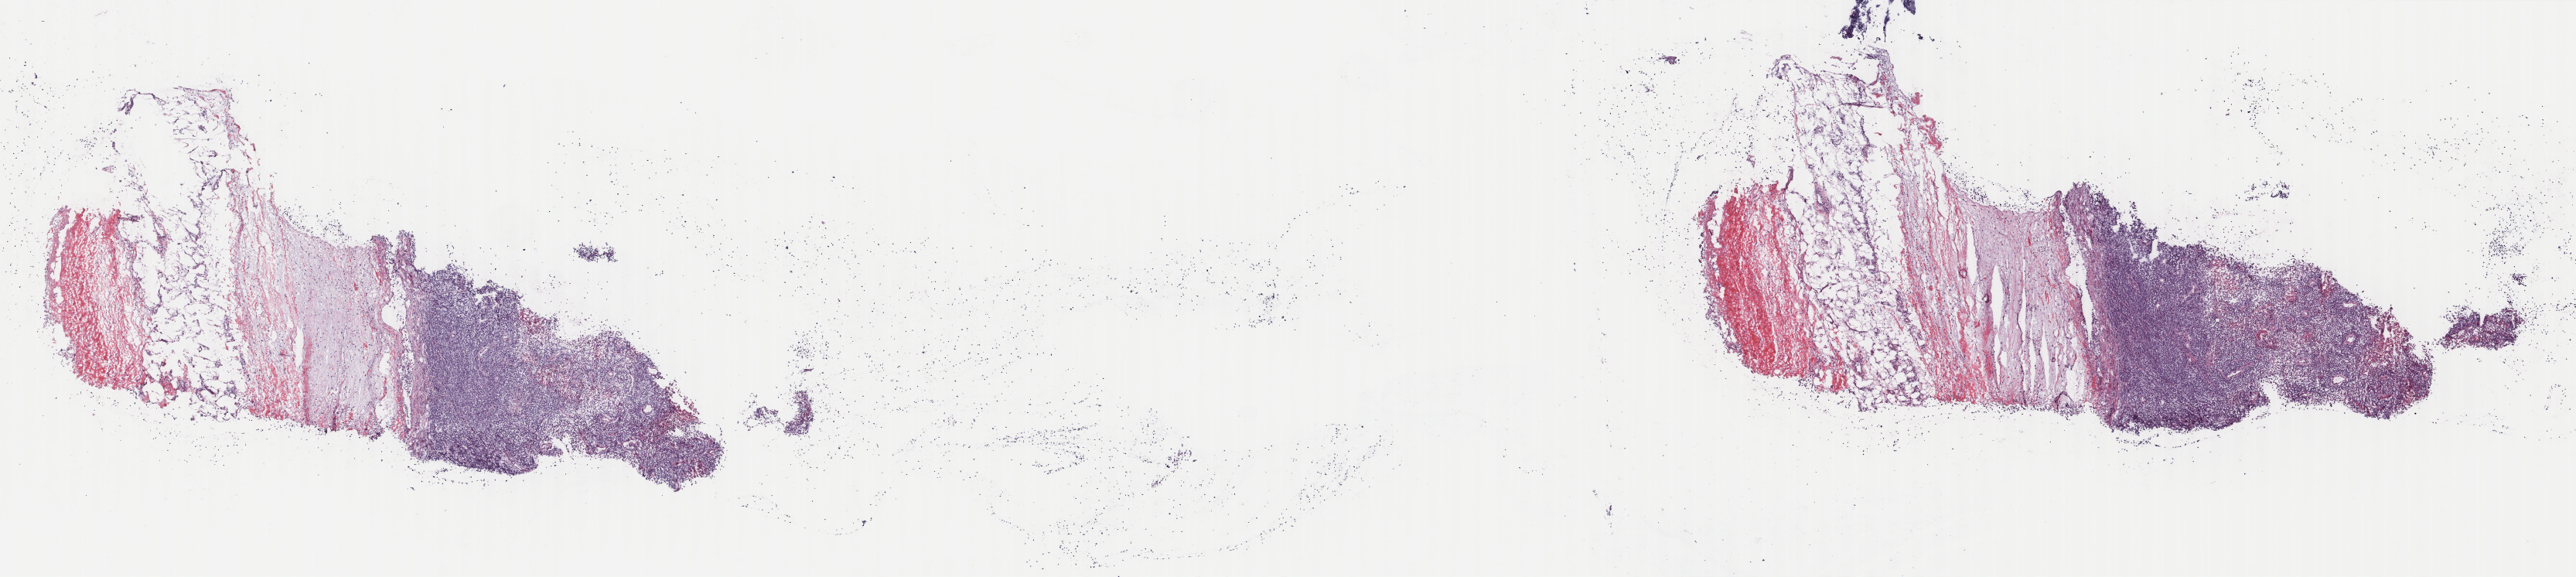
Digitized H&E-stained tissue section (whole slide), a low-resolution overview of the entire scanned area, about 26.4 x 5.9 mm, frozen section from the top of the tissue portion, metastatic tumour sample, sampled site not recorded. Female, age 34 years at initial diagnosis. Pathologist review of this section (percent, as recorded): tumour cells 40%, tumour nuclei 65%, normal cells 55%, stromal cells 0%, necrosis 5%. Infiltration values recorded for this section: lymphocyte infiltration 3%, monocyte infiltration 0%, neutrophil infiltration 0%.
This section: metastatic tumour tissue. Patient diagnosis: Malignant melanoma, NOS.